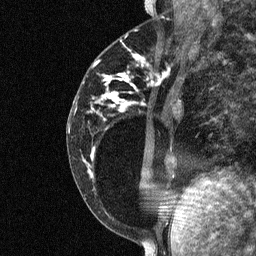
Breast MRI (dynamic contrast-enhanced), one sagittal slice. Position 26 of 64 along the scan axis. Dynamic contrast-enhanced study with each time point stored as its own series, time point 2 of 3 at this slice position (early post-contrast, ordered by acquisition time). 1.5 T. TE 4.8 ms, TR 27 ms. 2 mm slice thickness. 256 × 256 image matrix, field of view 180 × 180 mm. Female patient, age 34 years. Case-level facts recorded for this patient, not image findings: setting: breast cancer imaged before/during neoadjuvant chemotherapy; receptor status: HR-positive, HER2-negative.
Structures marked on this image (semi-automatic segmentation, software-assisted and operator-edited):
- analysis volume of interest (the breast-tissue region the enhancement analysis was run in; not a lesion): bounding box [x1, y1, x2, y2] px = [78, 44, 181, 191]
- tumour enhancement mask (voxels above the 90 % enhancement threshold inside the analysis volume of interest): [103, 83, 159, 107]